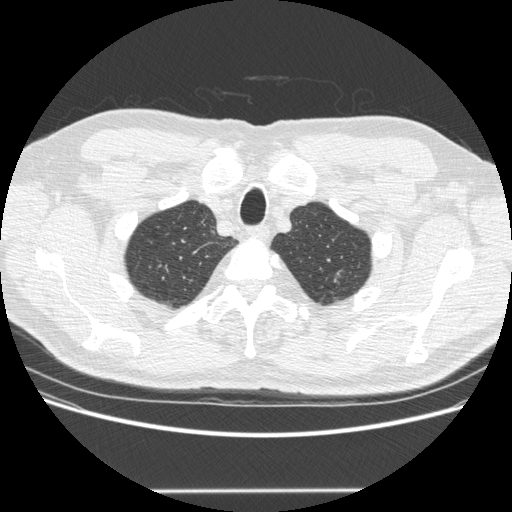
Low-dose screening chest CT, axial slice, second screening round (one year after baseline), lung window (W 1500 / L -600 HU), 1.25 mm slice thickness, standard (soft-tissue) reconstruction kernel (STANDARD), 120 kVp, 512 × 512 image matrix. Male participant, aged 69 years at enrolment. Former smoker at enrolment.
- Expert reader's lesion annotation, bounding box <312,263,346,294> (left, top, right, bottom; pixels).
- Screening reader's record for this exam: no non-calcified nodule ≥4 mm recorded.
- Official screen result: negative screen, significant abnormalities not suspicious for lung cancer.